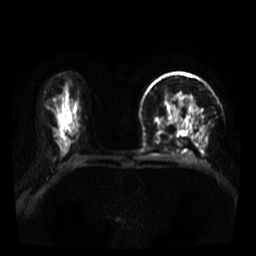
Breast MRI, one axial slice; slice 24 of 39 in the series (ordered by position); diffusion-weighted series; image 2 of 4 stored at this slice position (different b-values; order by instance number); 3 T; 256 × 256 image matrix, field of view 320 × 320 mm. Female patient.
Structures marked on this image (expert manual segmentation):
- tumour on diffusion-weighted imaging: box from (x=175, y=94) to (x=201, y=114) px